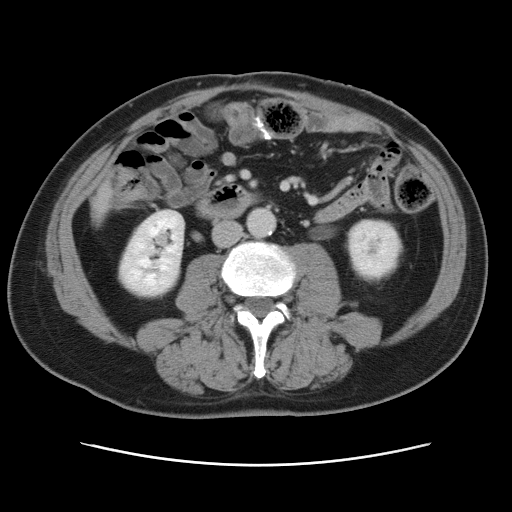
Contrast-enhanced abdominal CT, one axial slice; position 12 of 80 along the scan axis; 120 kVp; intravenous contrast given; soft-tissue window (W 400 / L 40 HU); 5 mm slice thickness; 512 × 512 image matrix, field of view 370 × 370 mm. Male patient, age 69 years. Case-level facts recorded for this patient, not image findings: diagnosis: colorectal cancer liver metastases, imaged before liver resection; multiple liver metastases: no; largest metastasis: 5 cm.
Outlined on this slice (manually delineated by an expert):
- liver: bounding box <93,180,110,216> (left, top, right, bottom; pixels)